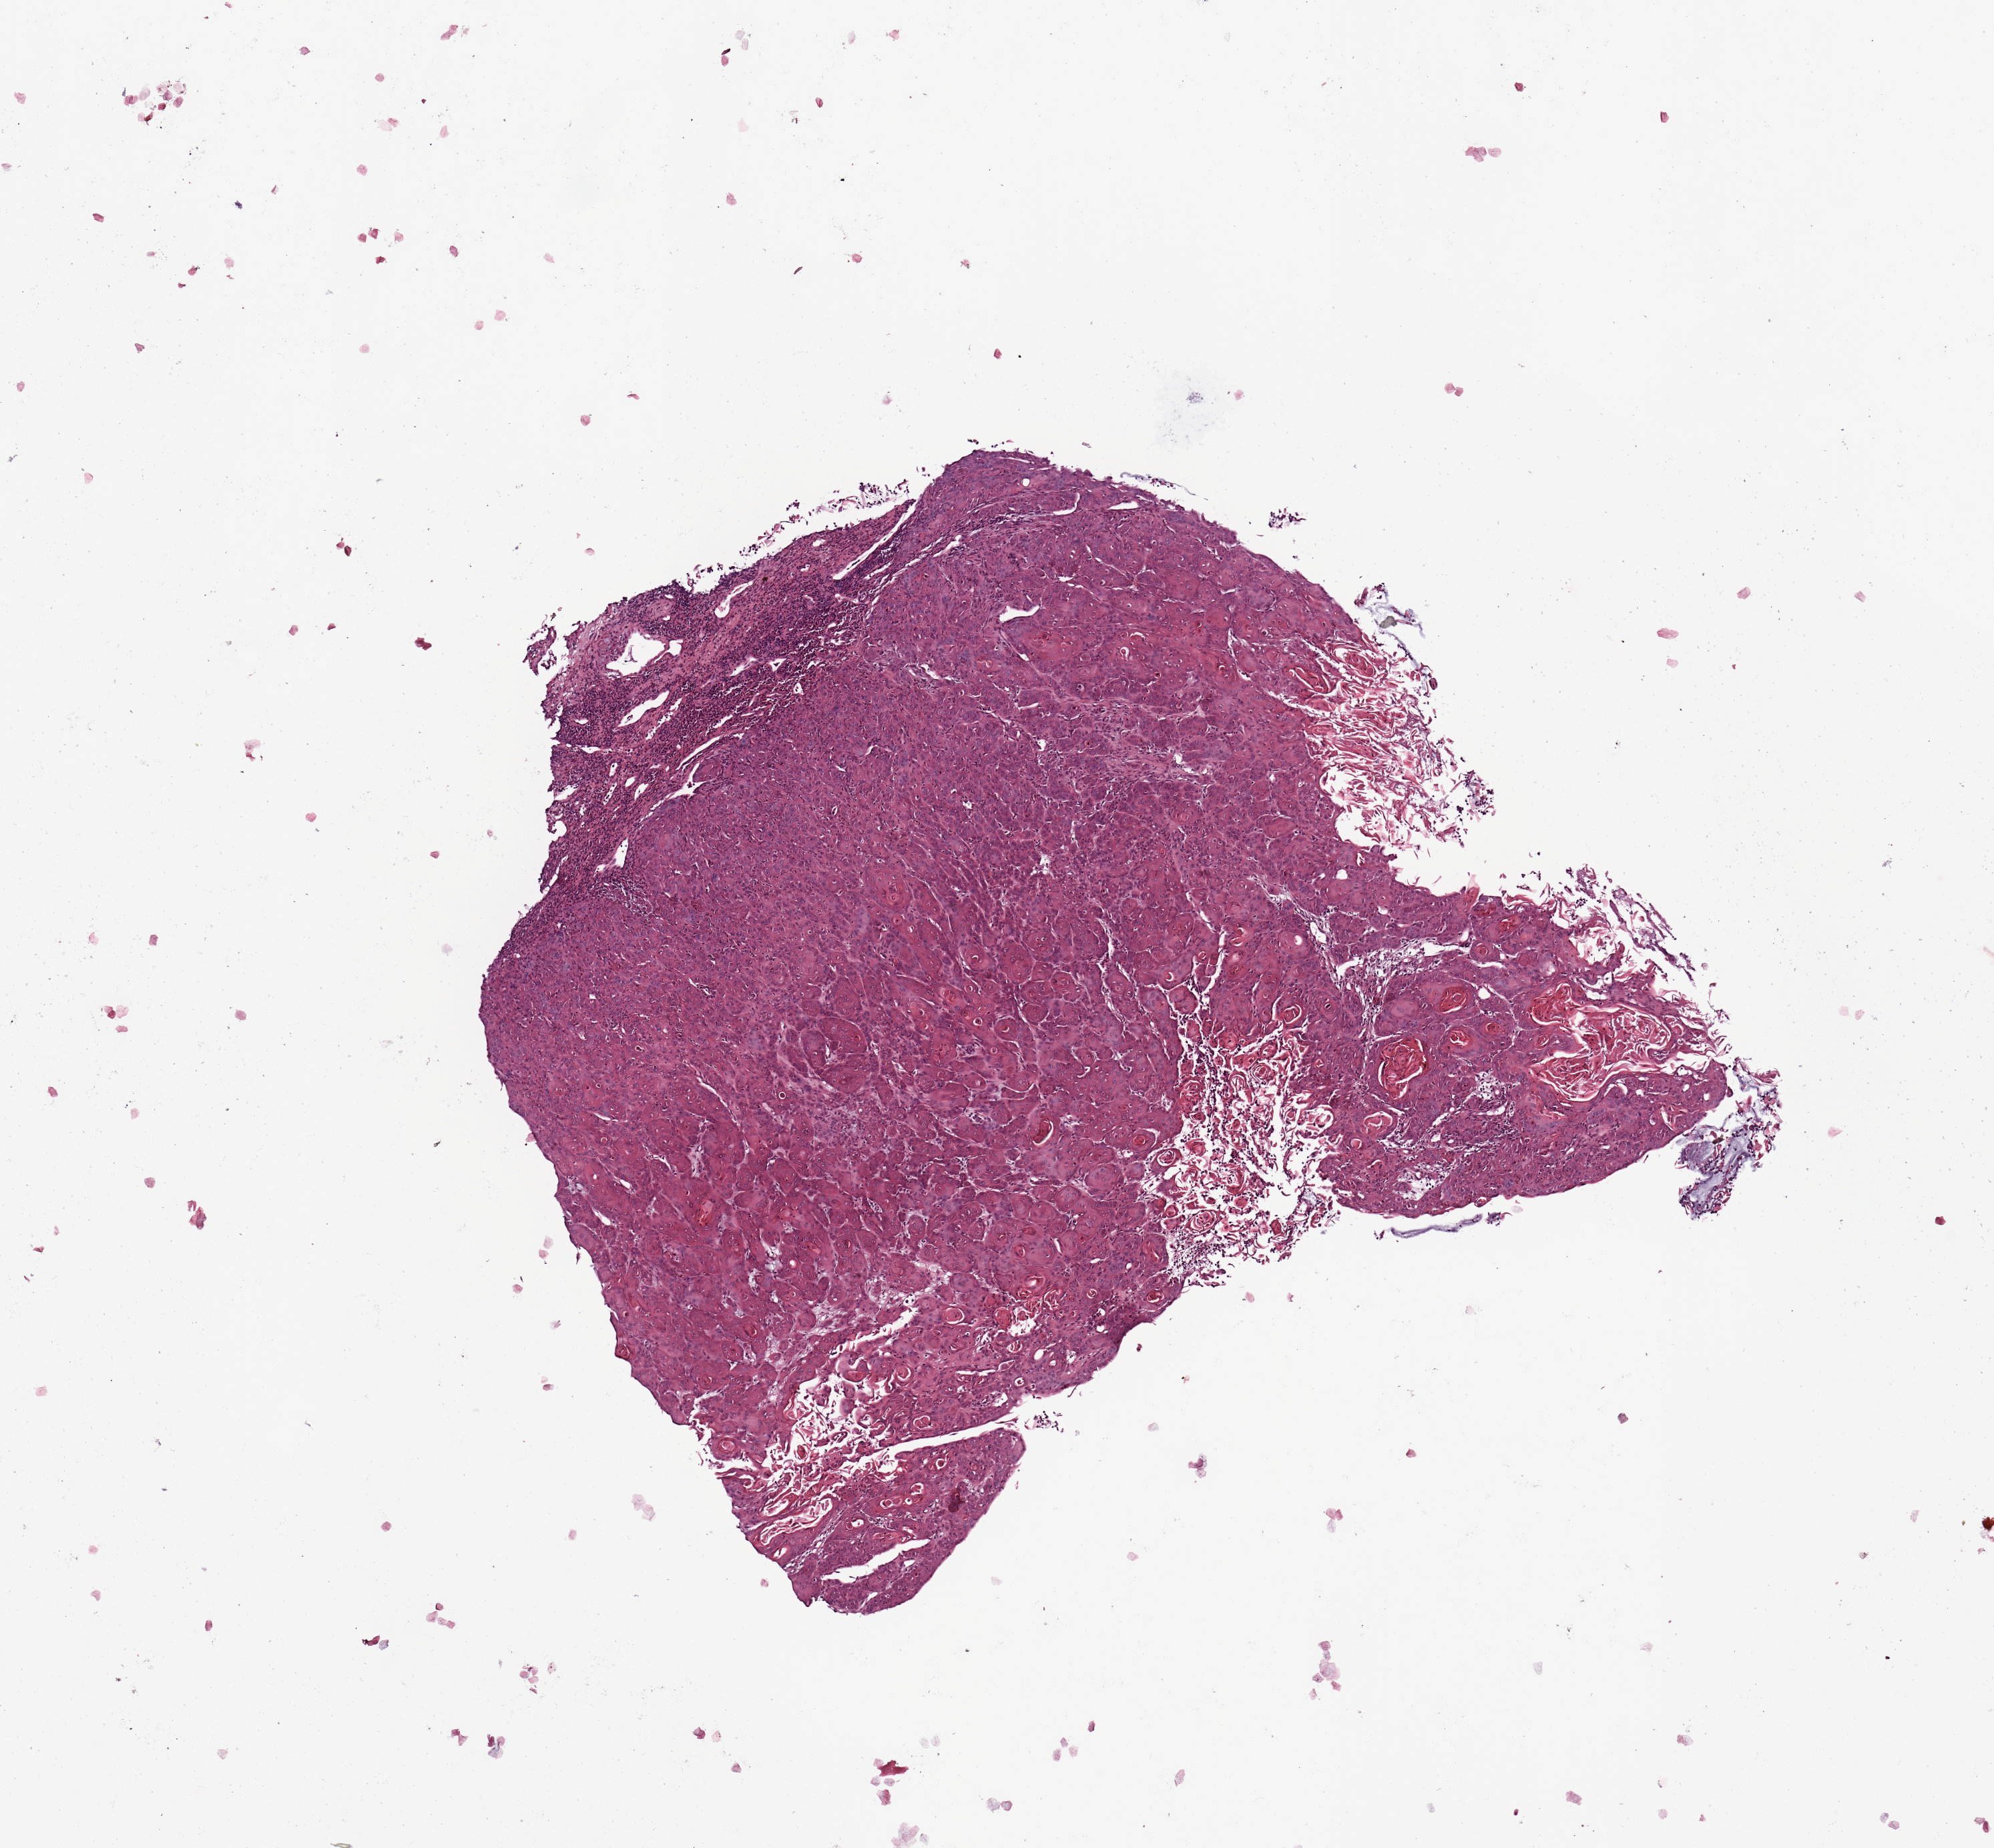
Hematoxylin and eosin (H&E) stained whole-slide image, shown as a low-resolution overview of the whole scanned area (about 5.9 x 5.5 mm, acquisition: 20x scan), tumour tissue sample, sampled site: larynx. Male, 52 y/o. Histologic grade: G1 (well differentiated). Pathologist review of this section (percent, as recorded): tumour nuclei 90%, necrosis 2%.
Primary tumour site (as recorded): larynx. Diagnosis: Squamous cell carcinoma, NOS (larynx, NOS). AJCC pathologic stage: IVA.